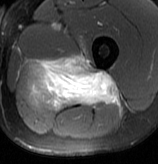
MRI of an extremity soft-tissue mass, one axial slice. Slice 47 of 70 in the series (ordered by position). T2-weighted fat-saturated. MR volume resampled by the dataset authors to the PET/CT grid (not the native acquisition matrix). 158 × 164 image matrix. Male patient. Case-level facts recorded for this patient, not image findings: histological type: extraskeletal osteosarcoma; grade: high; site of the primary tumour: left adductur.
Annotated regions visible in this slice (expert contour drawn on MRI and transferred to this co-registered scan by the dataset authors):
- gross tumour volume (mass): bounding box (x1, y1, x2, y2) in pixels: (29, 53, 119, 111)